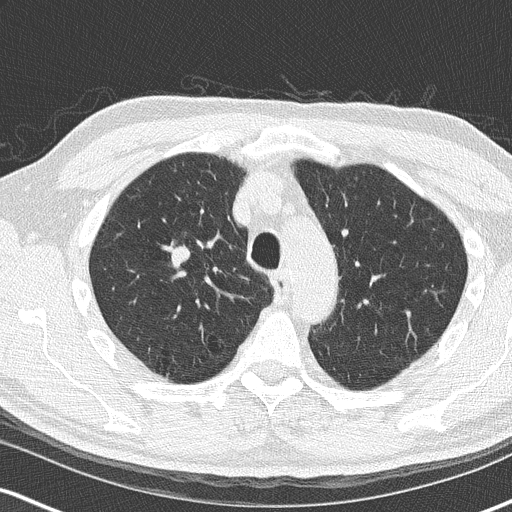
Axial slice from a low-dose chest CT screening exam, second annual screen, lung window (W 1500 / L -600 HU), slice 54 of 170 in the series, 512 × 512 image matrix, field of view 320 × 320 mm. Male participant, aged 68 years at enrolment. Current smoker at enrolment.
• Lesion marked by an expert reader, box from (x=152, y=230) to (x=216, y=291) px.
• Reader record for this screening exam (exam-level; its link to the box is not recorded): non-calcified nodule or mass ≥4 mm, right upper lobe, 18 × 15 mm, smooth margins, soft tissue attenuation, pre-existing on the prior screen: no.
• Official screen result: positive, change unspecified: nodule(s) >= 4 mm or enlarging nodule(s), mass(es), or other non-specific abnormalities suspicious for lung cancer.
• Later outcome: lung cancer diagnosed 136 days after this screen — small cell carcinoma, NOS, right upper lobe, stage IIIB (AJCC 6th edition), 20 mm at pathology.